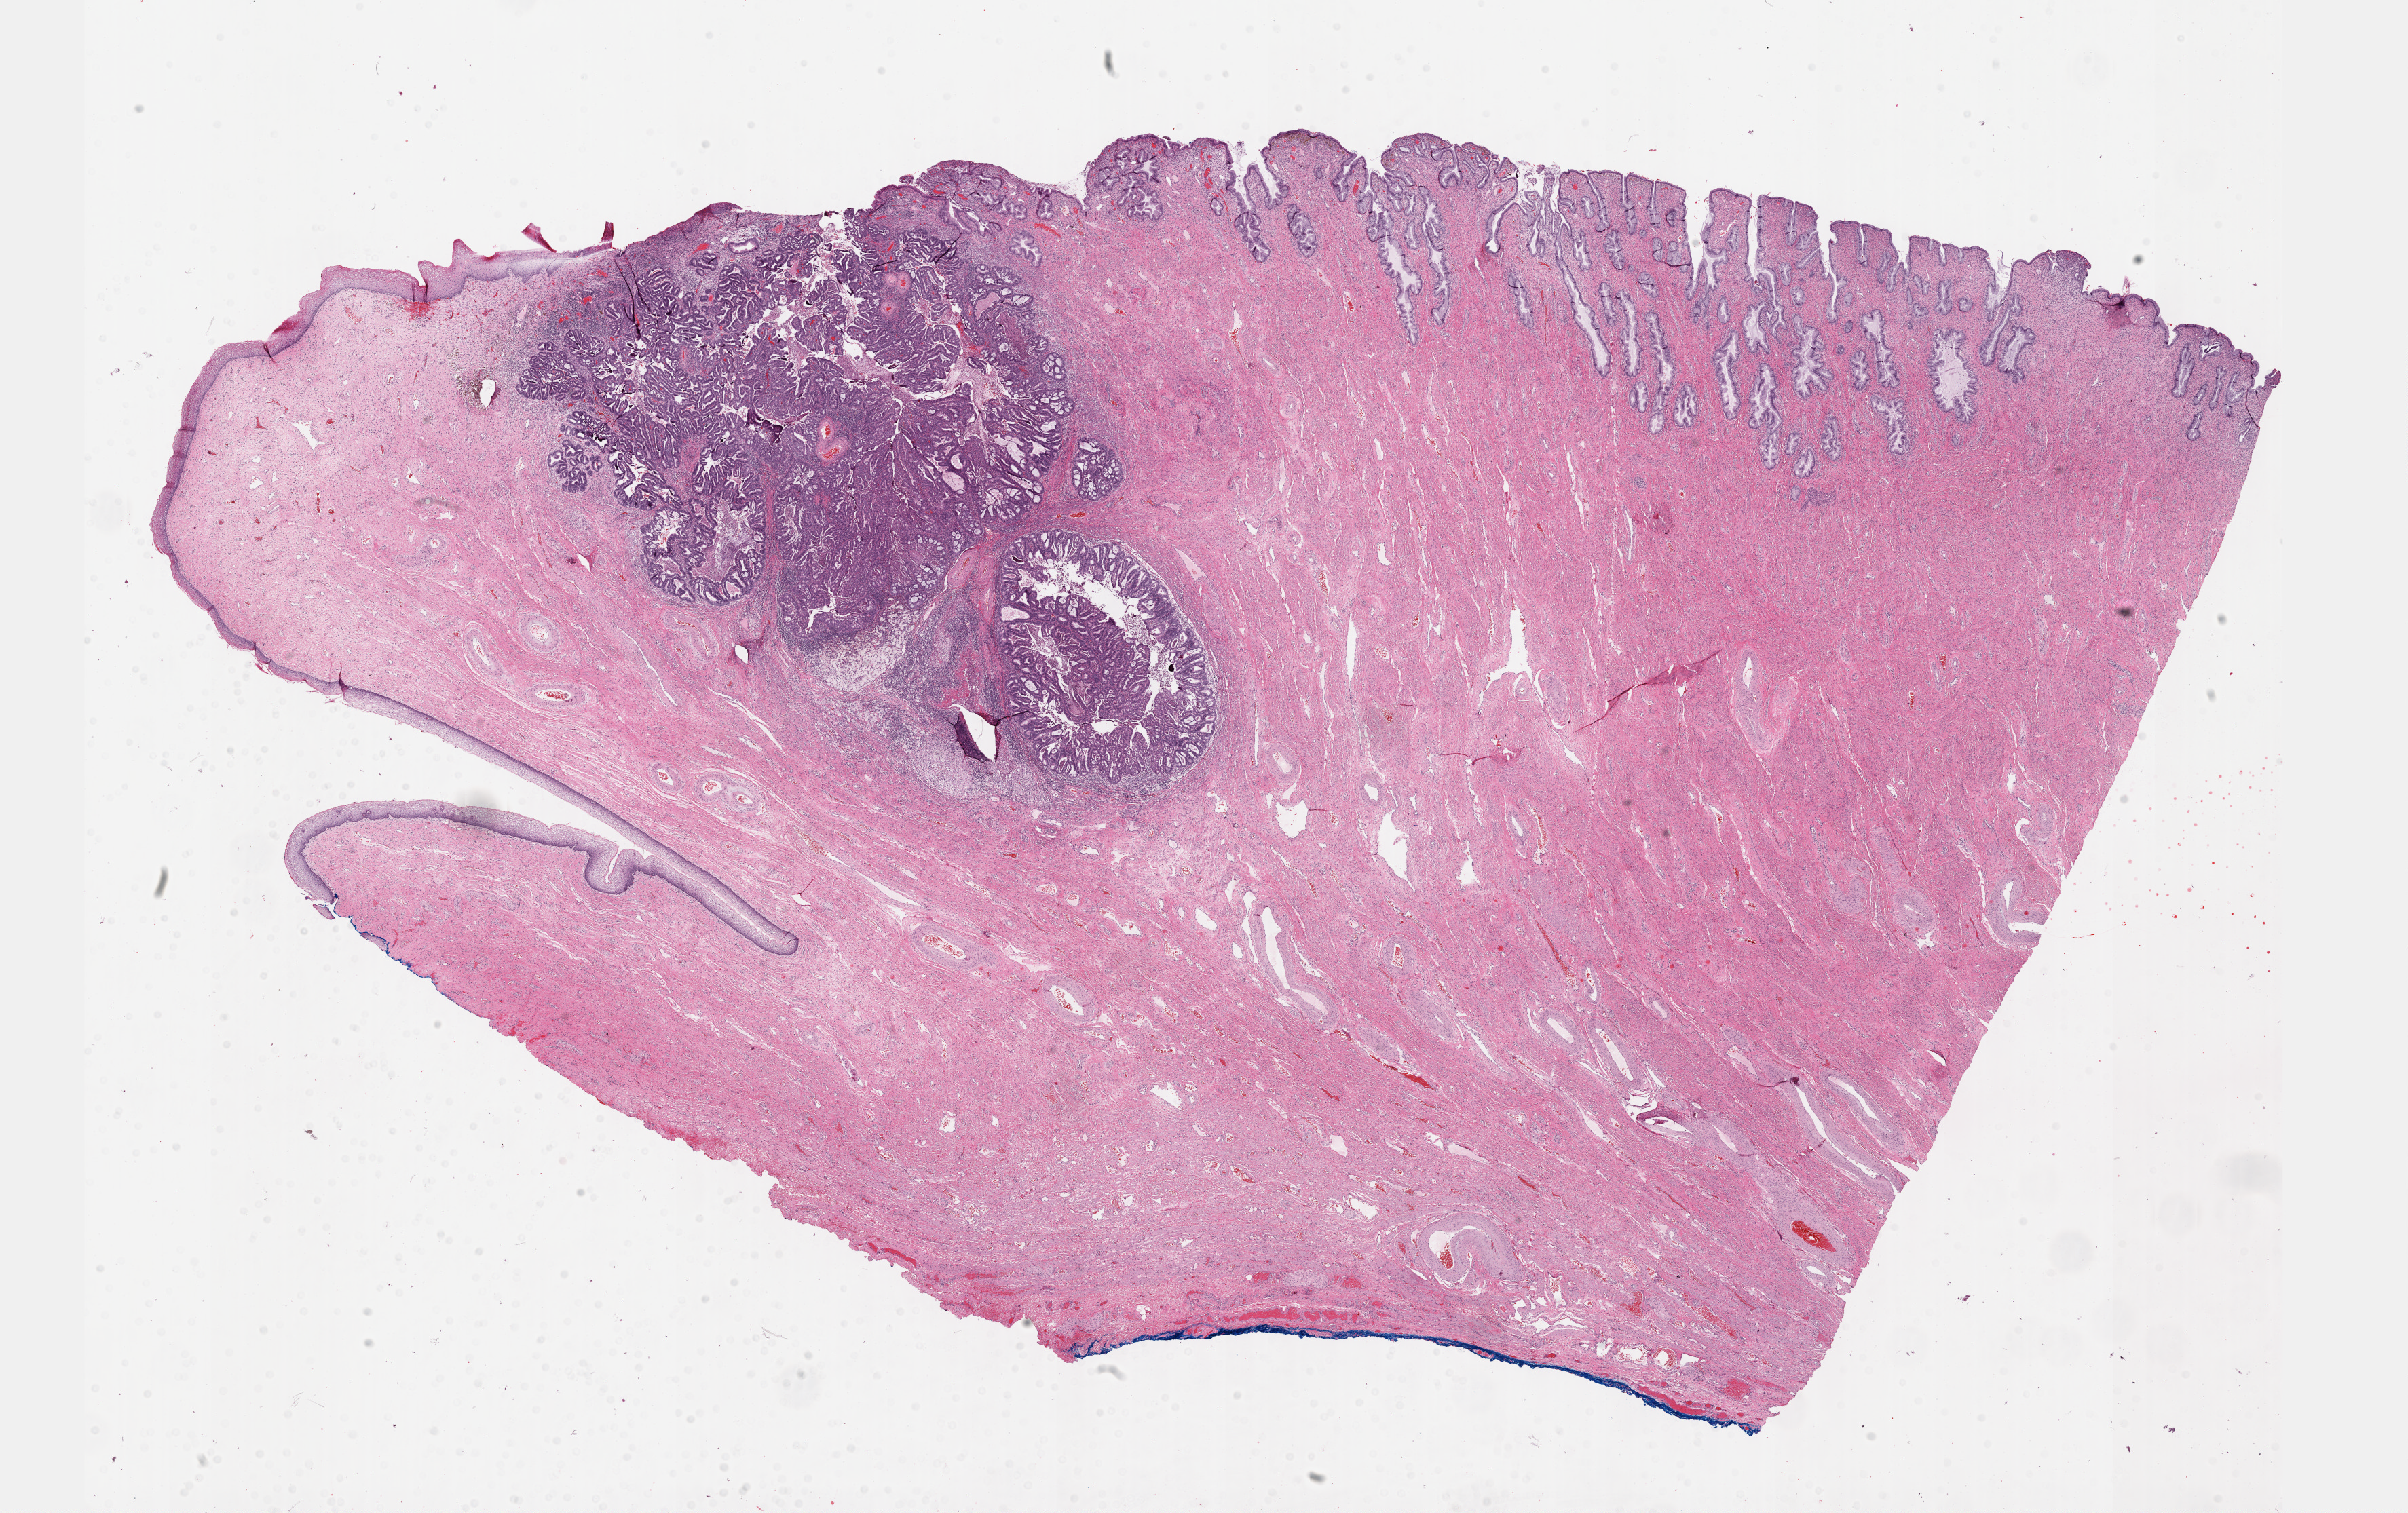
H&E-stained whole-slide image, low-resolution overview of the scanned area, about 28.7 x 18.0 mm; FFPE section; primary tumour sample from the cervix. Female patient; age at initial diagnosis 36 years. Histologic grade: G2 (moderately differentiated).
• FIGO stage: IB1
• diagnosis: Mucinous adenocarcinoma, endocervical type (endocervix)